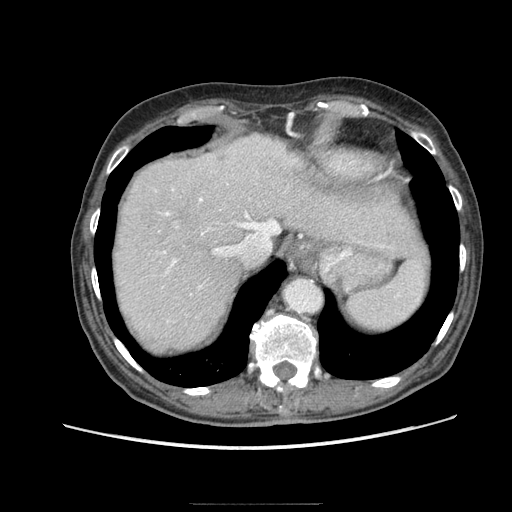
Contrast-enhanced abdominal CT (liver protocol), one axial slice; slice 68 of 83 in the series (ordered by position); reconstruction kernel STANDARD; soft-tissue window (W 400 / L 40 HU); 2.5 mm slice thickness; 512 × 512 image matrix. From the clinical record (not read from this slice): diagnosis: hepatocellular carcinoma (patient treated with transarterial chemoembolisation; whether this scan precedes or follows treatment is not stated here); TNM stage (as recorded): Stage-I; Child-Pugh class: A; tumour differentiation: moderately differentiated; tumour nodularity: uninodular.
Annotated regions visible in this slice (semi-automatic segmentation, software-assisted and operator-edited):
- abdominal aorta: bounding box (x1, y1, x2, y2) in pixels: (284, 279, 323, 313)
- liver parenchyma outside the tumour (the mass and vessels are separate outlines, so this box may not span the whole liver): (114, 134, 346, 352)
- liver vessels: (164, 189, 249, 288)